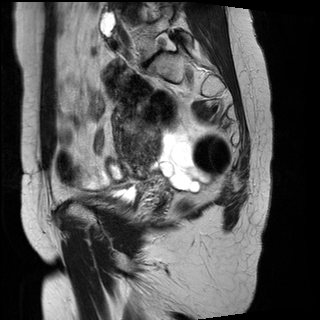
Pelvic MRI for cervical cancer, one sagittal slice; position 20 of 29 along the scan axis; T2-weighted; 1.5 T; TE 89 ms, TR 2930 ms; 4 mm slice thickness; 320 × 320 image matrix, field of view 260 × 260 mm. Patient: female, 45 years.
Outlined on this slice (manually delineated by an expert):
- uterus and cervix: box from (x=113, y=111) to (x=162, y=170) px